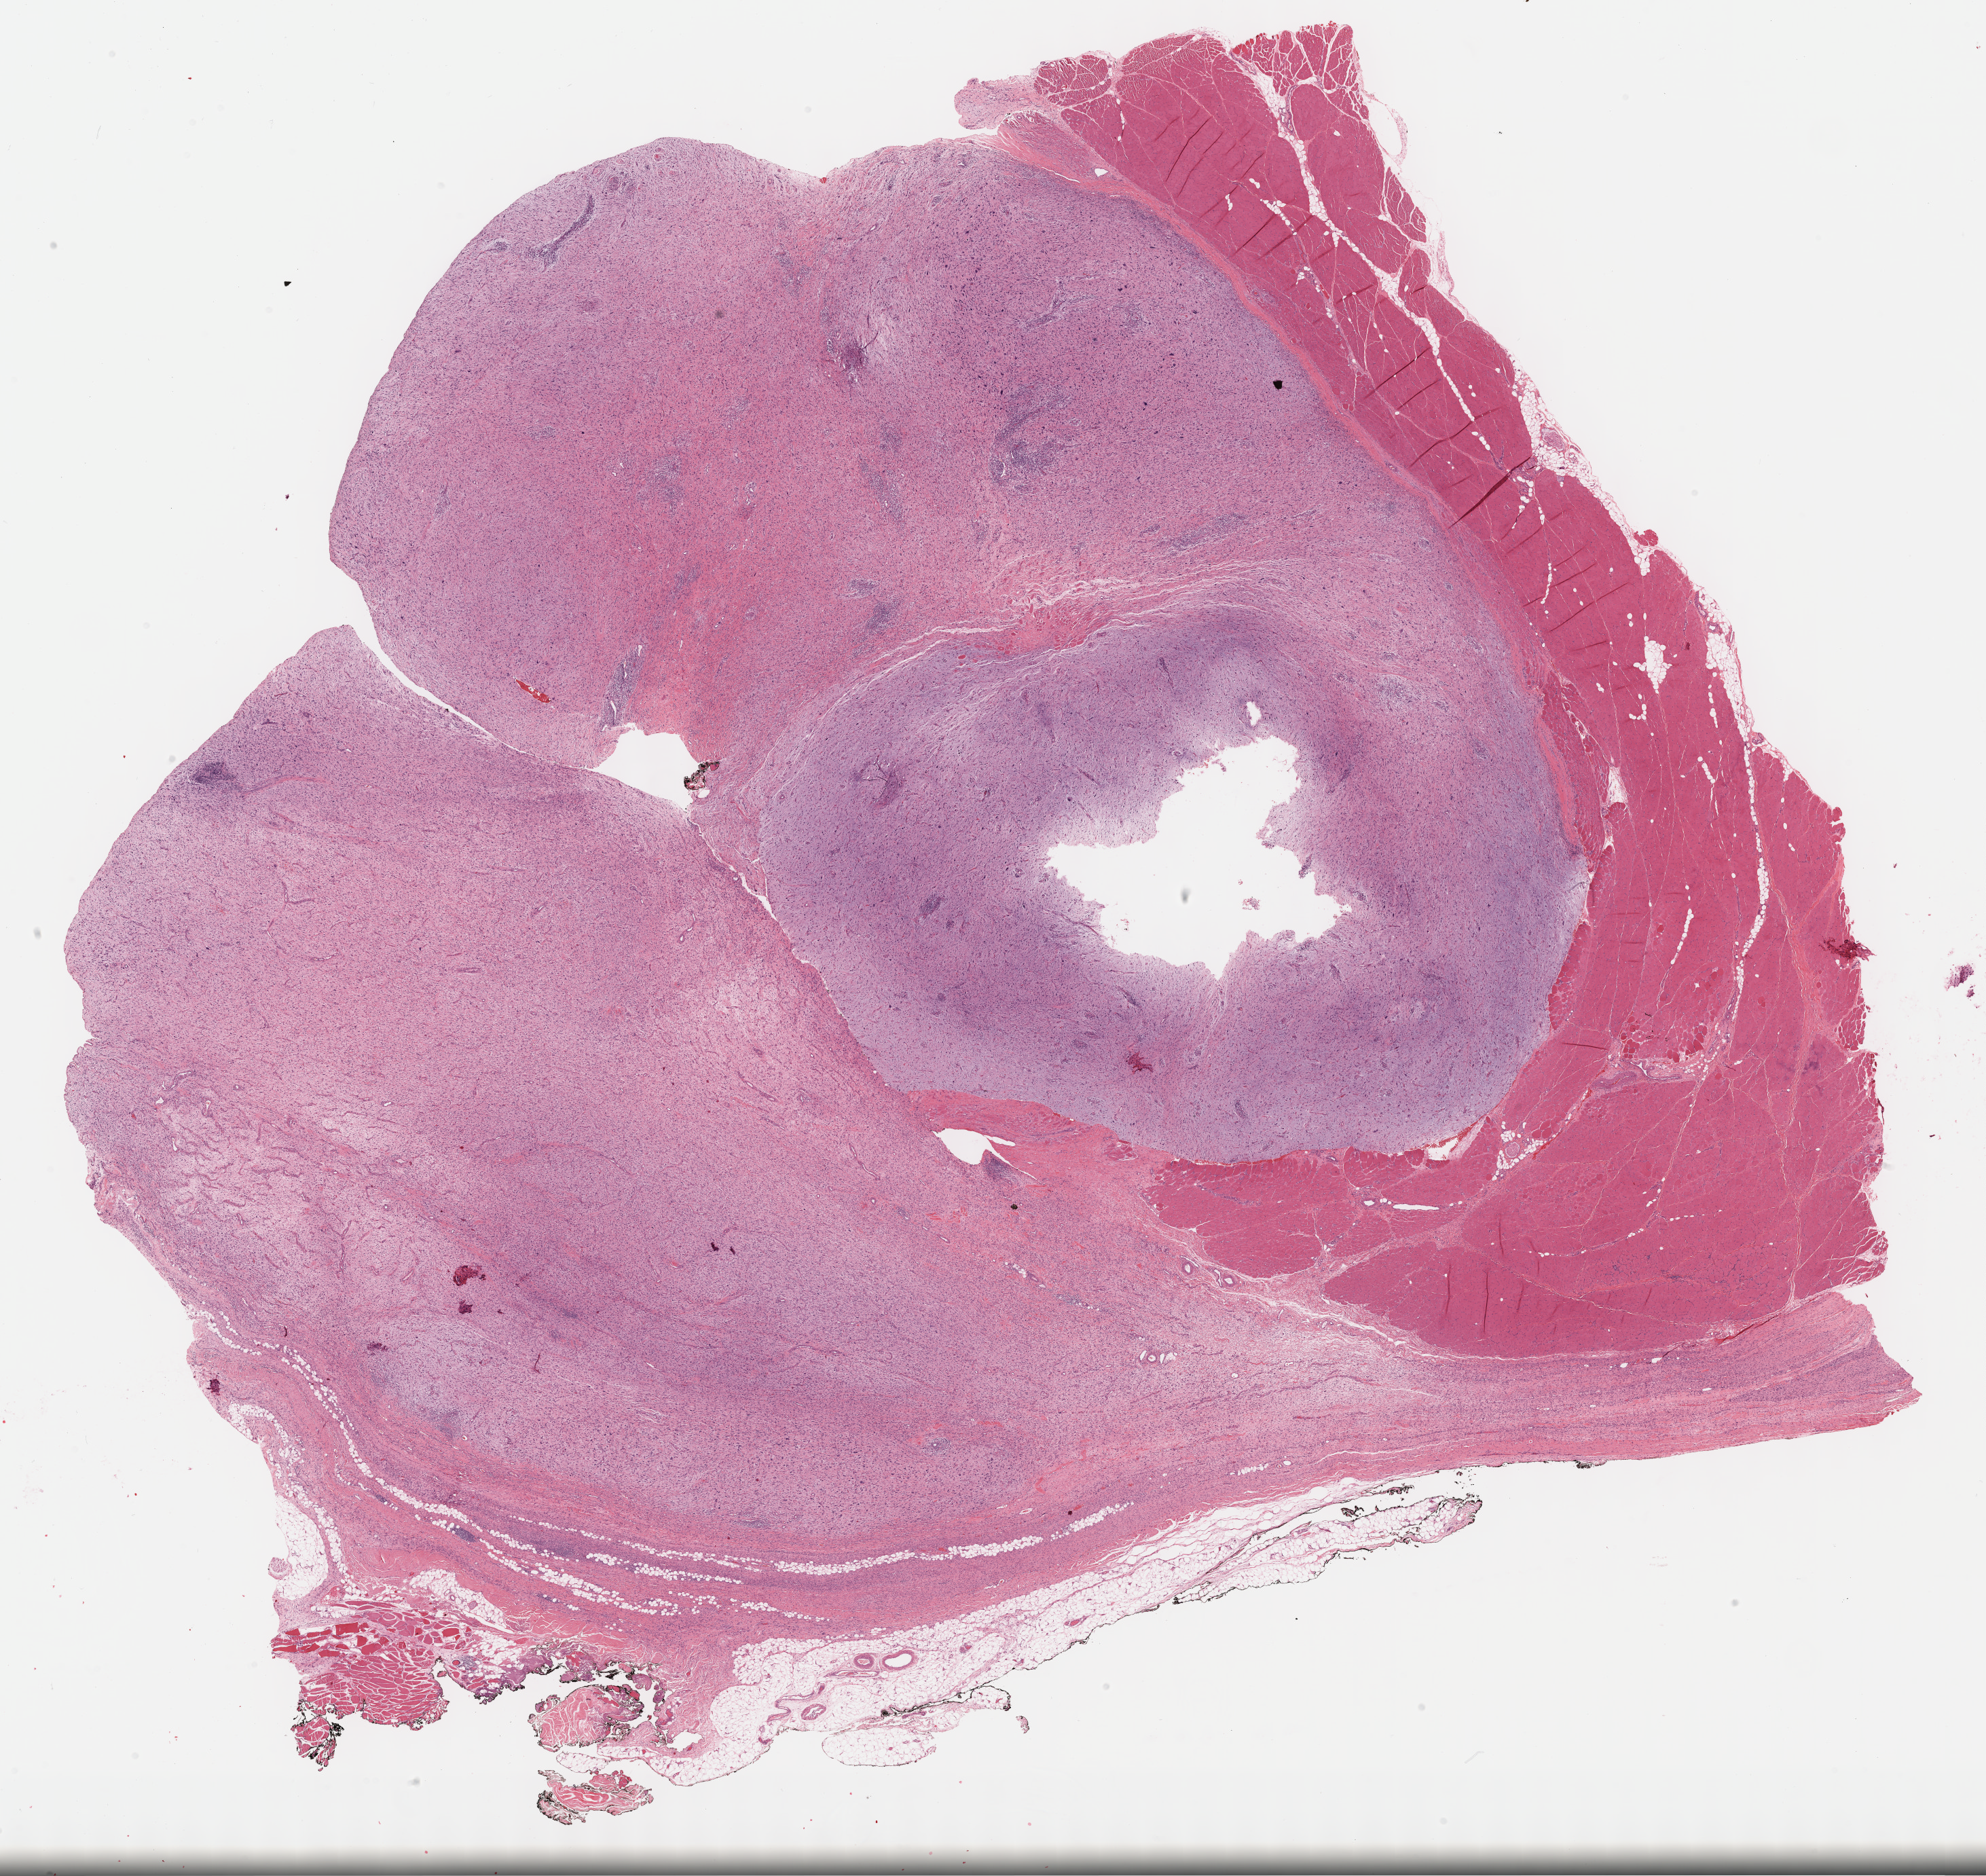
Whole-slide histology image, H&E-stained — a low-resolution overview of the entire scanned area, about 23.7 x 22.3 mm (from a 40x scan), formalin-fixed paraffin-embedded (FFPE) diagnostic section, primary tumour sample from the connective, subcutaneous and other soft tissues. Patient: female, age at initial diagnosis 78 years.
Histologic diagnosis: Fibromyxosarcoma (connective, subcutaneous and other soft tissues of lower limb and hip).